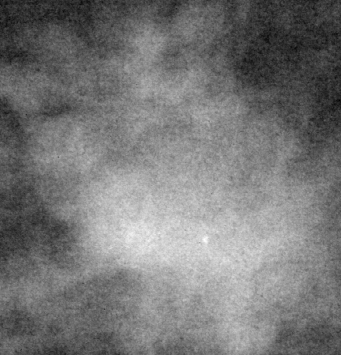
Cropped region of a digitized screen-film mammogram centred on a radiologist-marked abnormality; right breast; MLO view.
Mass, shape lobulated, margins circumscribed / ill defined; BI-RADS assessment category 4; subtlety rating 4 on a 1 (subtle) to 5 (obvious) scale; pathology (as recorded): malignant.